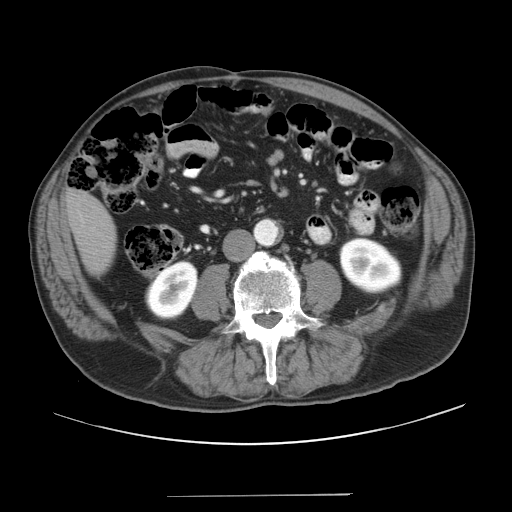
Contrast-enhanced abdominal CT, one axial slice; slice 1 of 41 in the series (ordered by position); 120 kVp; intravenous contrast given; soft-tissue window (W 400 / L 40 HU); 5 mm slice thickness; 512 × 512 image matrix, field of view 420 × 420 mm. Male patient, age 75 years. From the clinical record (not read from this slice): diagnosis: colorectal cancer liver metastases, imaged before liver resection; multiple liver metastases: no; largest metastasis: 5.2 cm; disease in both lobes: no.
Structures marked on this image (manually delineated by an expert):
- liver: bounding box (x1, y1, x2, y2) in pixels: (69, 190, 116, 274)
- planned liver remnant (the part of the liver to remain after resection): (69, 190, 117, 274)